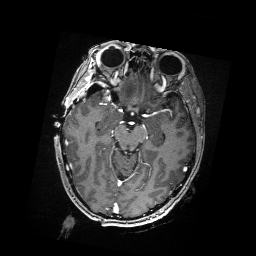
Brain MRI from a brain-tumour surgery series, one axial slice; position 108 of 176 along the scan axis; T1-weighted post-contrast; 1 mm slice thickness; 256 × 256 image matrix, field of view 256 × 256 mm. Case-level facts recorded for this patient, not image findings: histopathology: Metastatic Carcinoma from Breast primary.
Outlined on this slice (manually delineated by an expert):
- residual tumour: bounding box <98,90,105,96> (left, top, right, bottom; pixels)